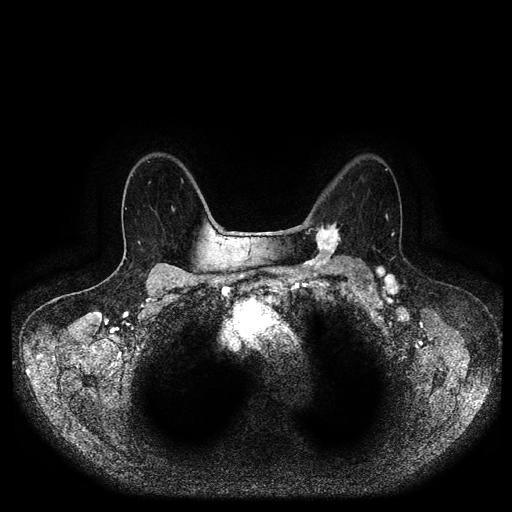
Breast MRI (dynamic contrast-enhanced, multi-phase), one axial slice. Dynamic contrast-enhanced series, time point 2 of 5 at this slice position (early post-contrast). 1.5 T. TE 2.6 ms, TR 5.2 ms. 512 × 512 image matrix, field of view 380 × 380 mm. Patient: female, 69 years.
Outlined on this slice (semi-automatically segmented with operator editing):
- breast lesion (labelled 'tumour' in the annotation; benign lesions carry a separate 'benign' label): bounding box (x1, y1, x2, y2) in pixels: (302, 221, 343, 272)